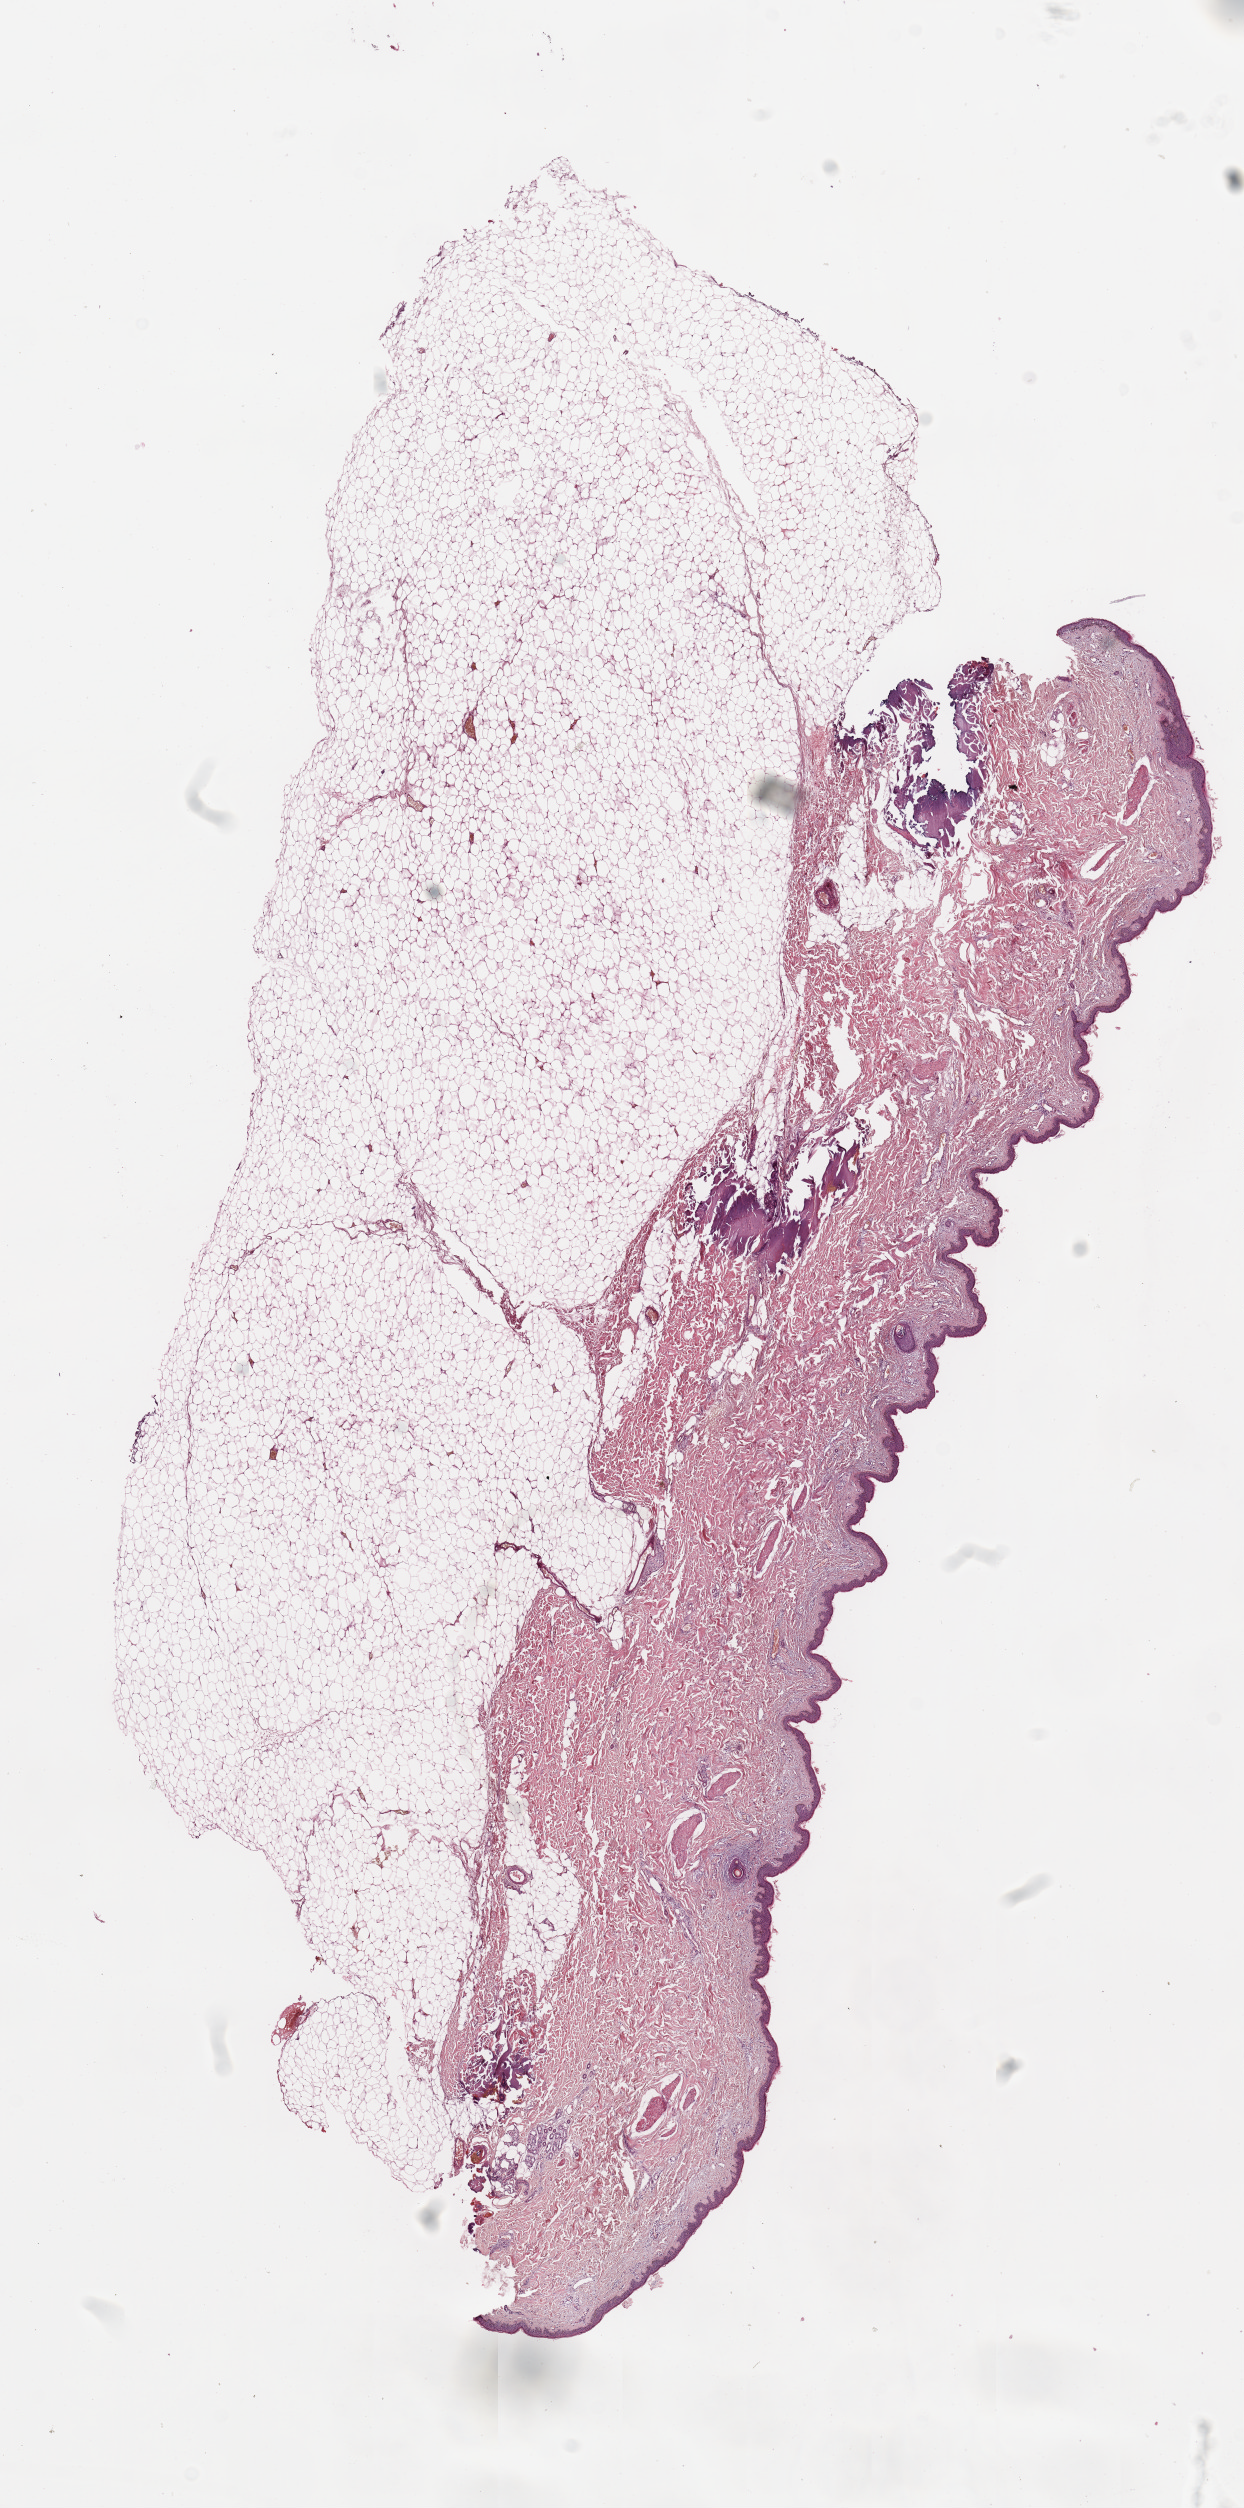
Hematoxylin and eosin (H&E) stained whole-slide image, whole scanned area (about 9.8 x 19.8 mm, slide scanned at 20x) shown as a low-resolution overview, normal (non-tumour) tissue sample. Female, 43 y/o.
This section: normal (non-tumour) tissue from the same patient. Patient diagnosis (cohort enrolment): sarcoma (site not recorded at cohort level).